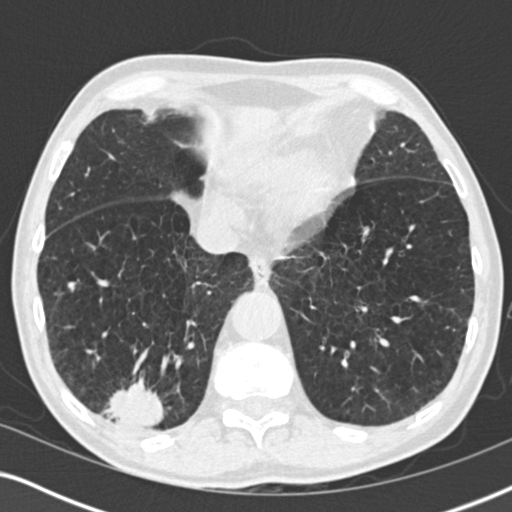
Axial slice from a low-dose chest CT screening exam; baseline screening round; lung window (W 1500 / L -600 HU); 2 mm slice thickness; 120 kVp; slice 138 of 196 in the series; 512 × 512 image matrix. Male, age 64 years at enrolment. Former smoker at enrolment.
Expert reader's lesion annotation, bounding box [x1, y1, x2, y2] px = [84, 369, 179, 448]. The screening reader recorded 3 non-calcified nodules or masses ≥4 mm on this exam (lingula, lingula, right lower lobe); which of them this box marks is not recorded. Lung cancer was diagnosed 27 days after this screen: squamous cell carcinoma, NOS, right lower lobe, moderately differentiated (G2), stage IV (AJCC 6th edition), 40 mm at pathology.